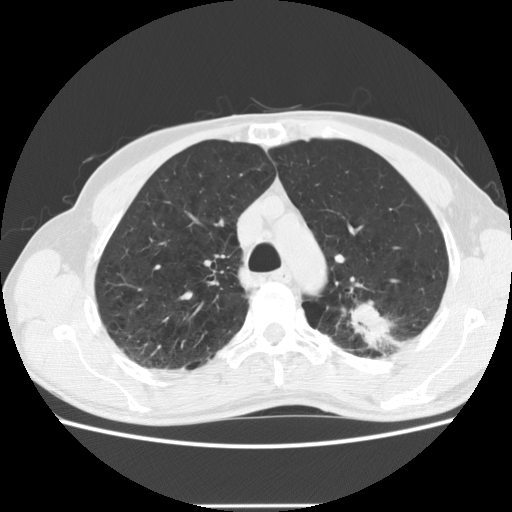
Low-dose screening chest CT, one axial slice; position 145 of 191 along the scan axis; 120 kVp; lung window (W 1500 / L -600 HU); 512 × 512 image matrix, field of view 352 × 352 mm.
Annotated regions visible in this slice (outlined manually by an expert reader):
- lesion 1 (tumor, upper lobe of left lung): bounding box [x1, y1, x2, y2] px = [350, 303, 391, 348]